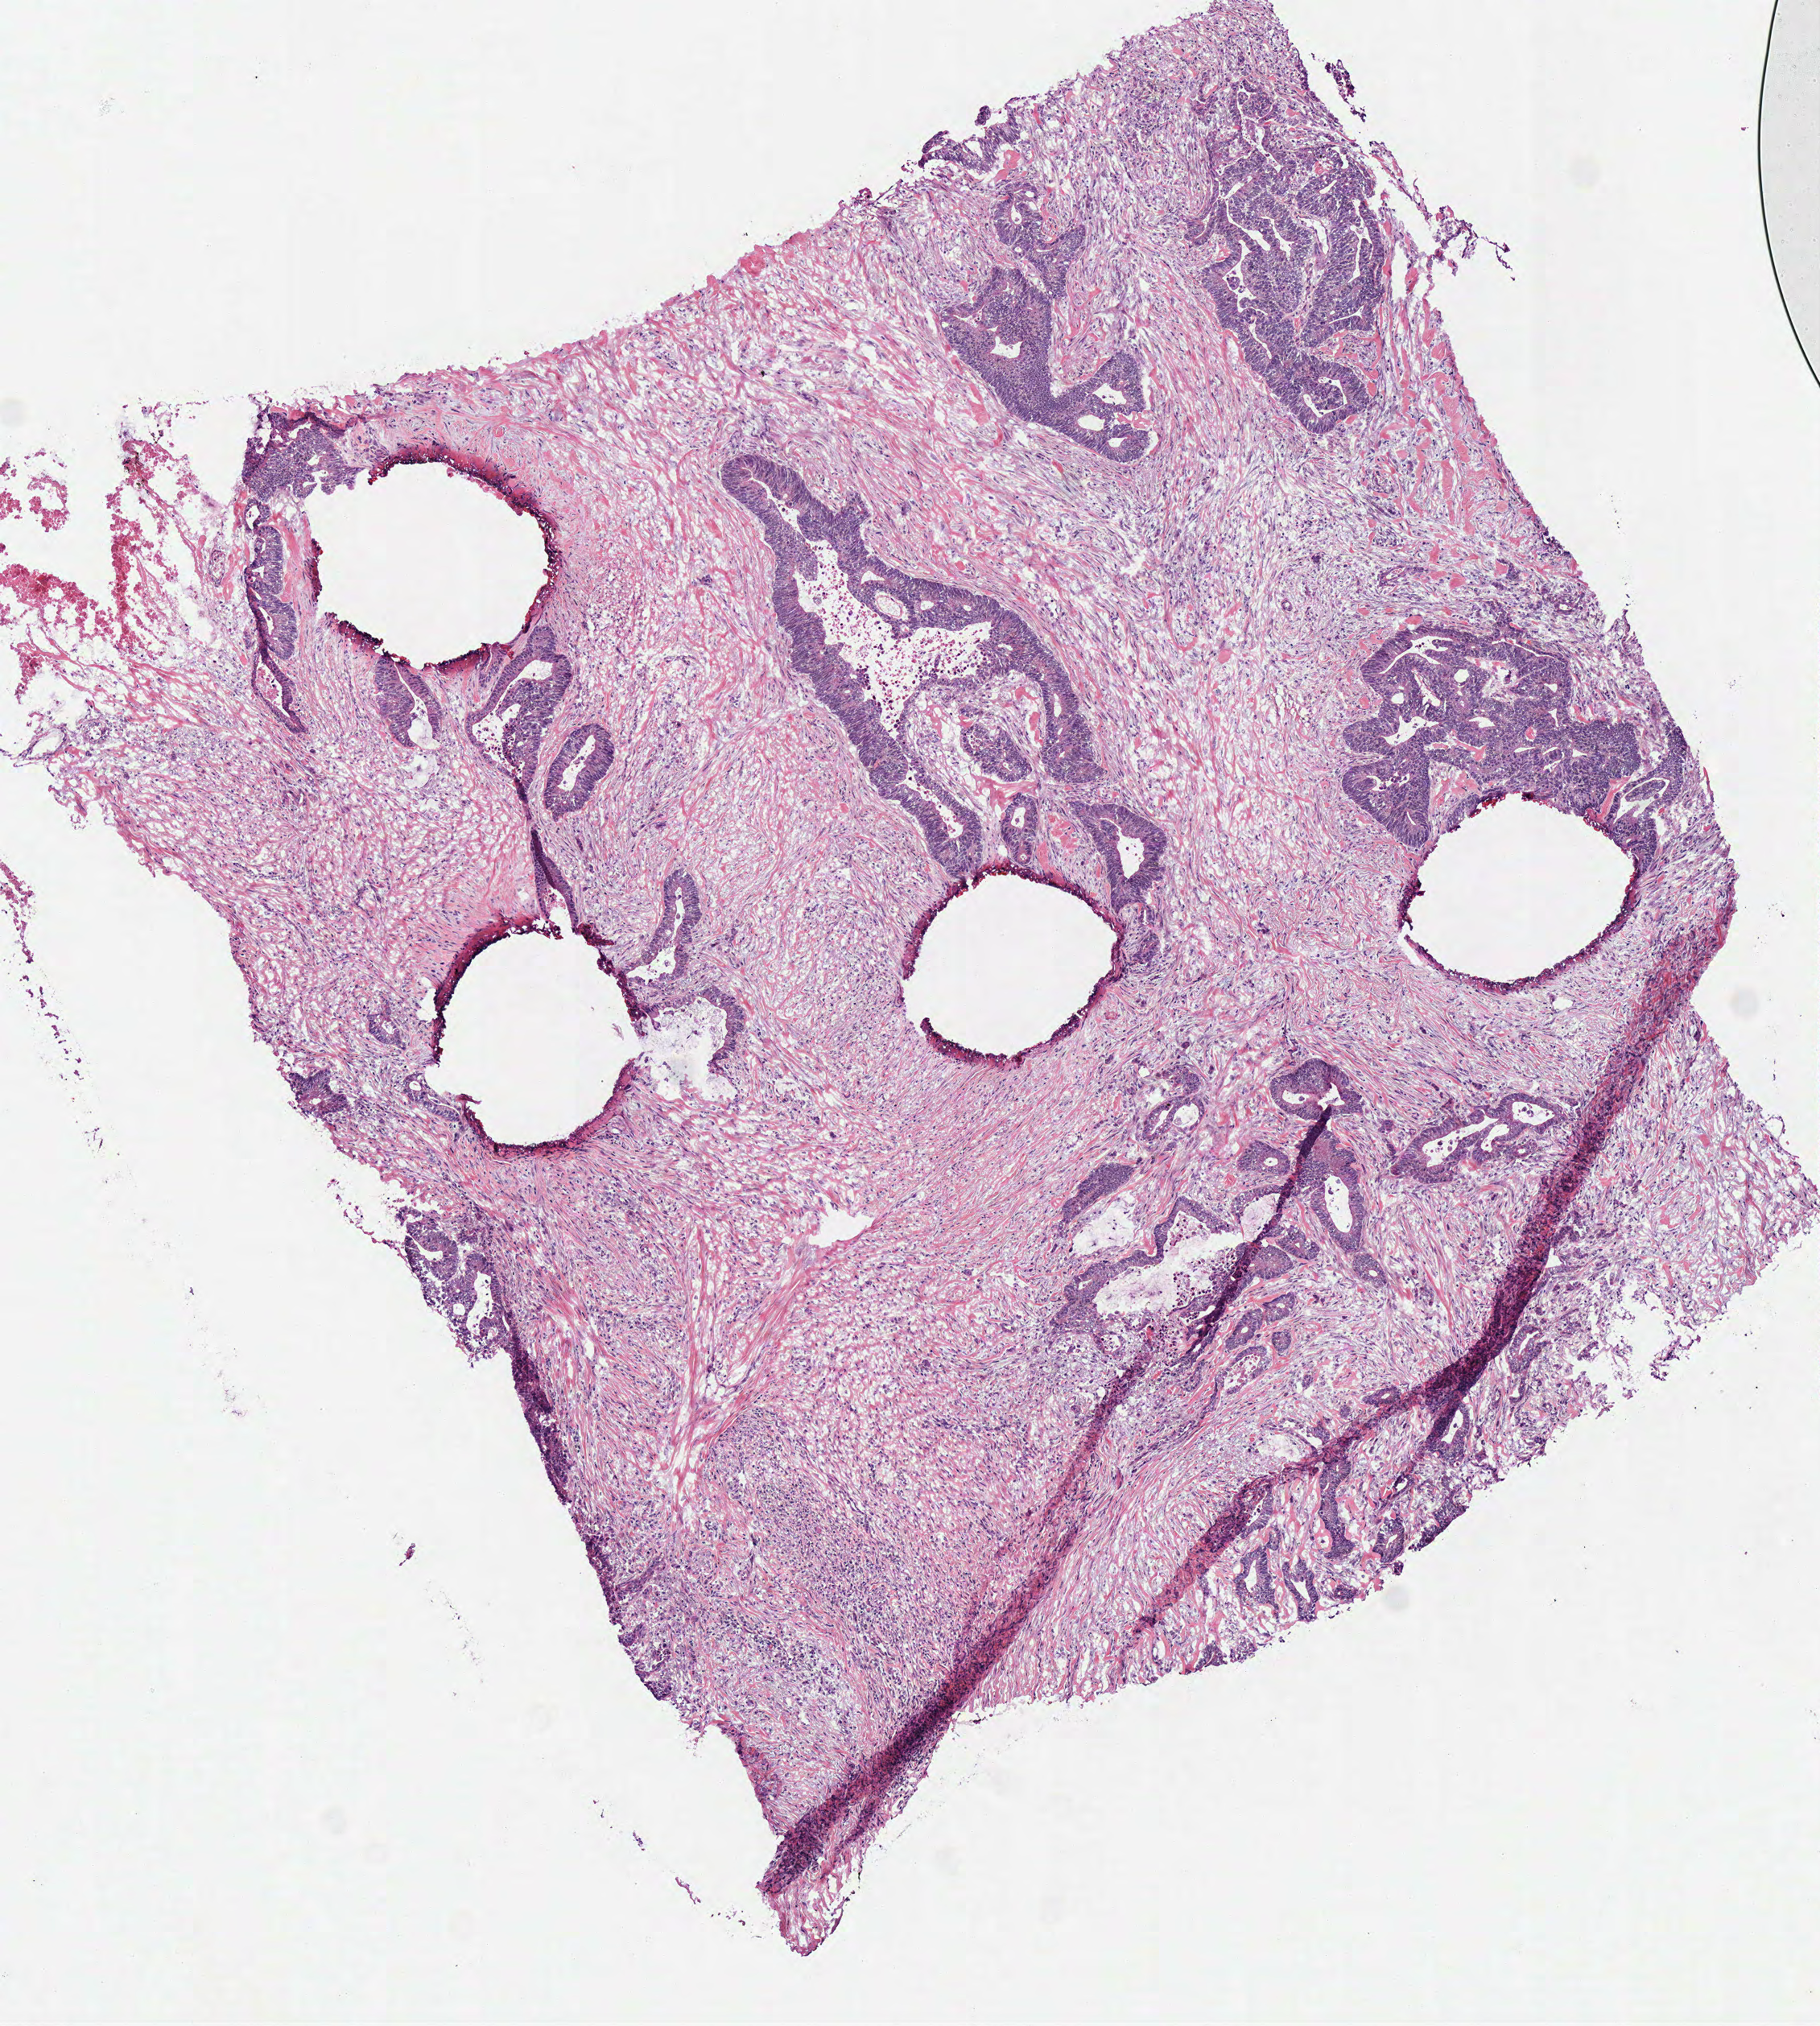
Digitized Hematoxylin and eosin (H&E) stained tissue section (whole slide), whole scanned area (about 4.5 x 5.0 mm, from a 40x scan) shown as a low-resolution overview; frozen section; primary tumour sample from the colon. Male, age 78 years at initial diagnosis.
Histologic diagnosis: Adenocarcinoma, NOS (cecum).